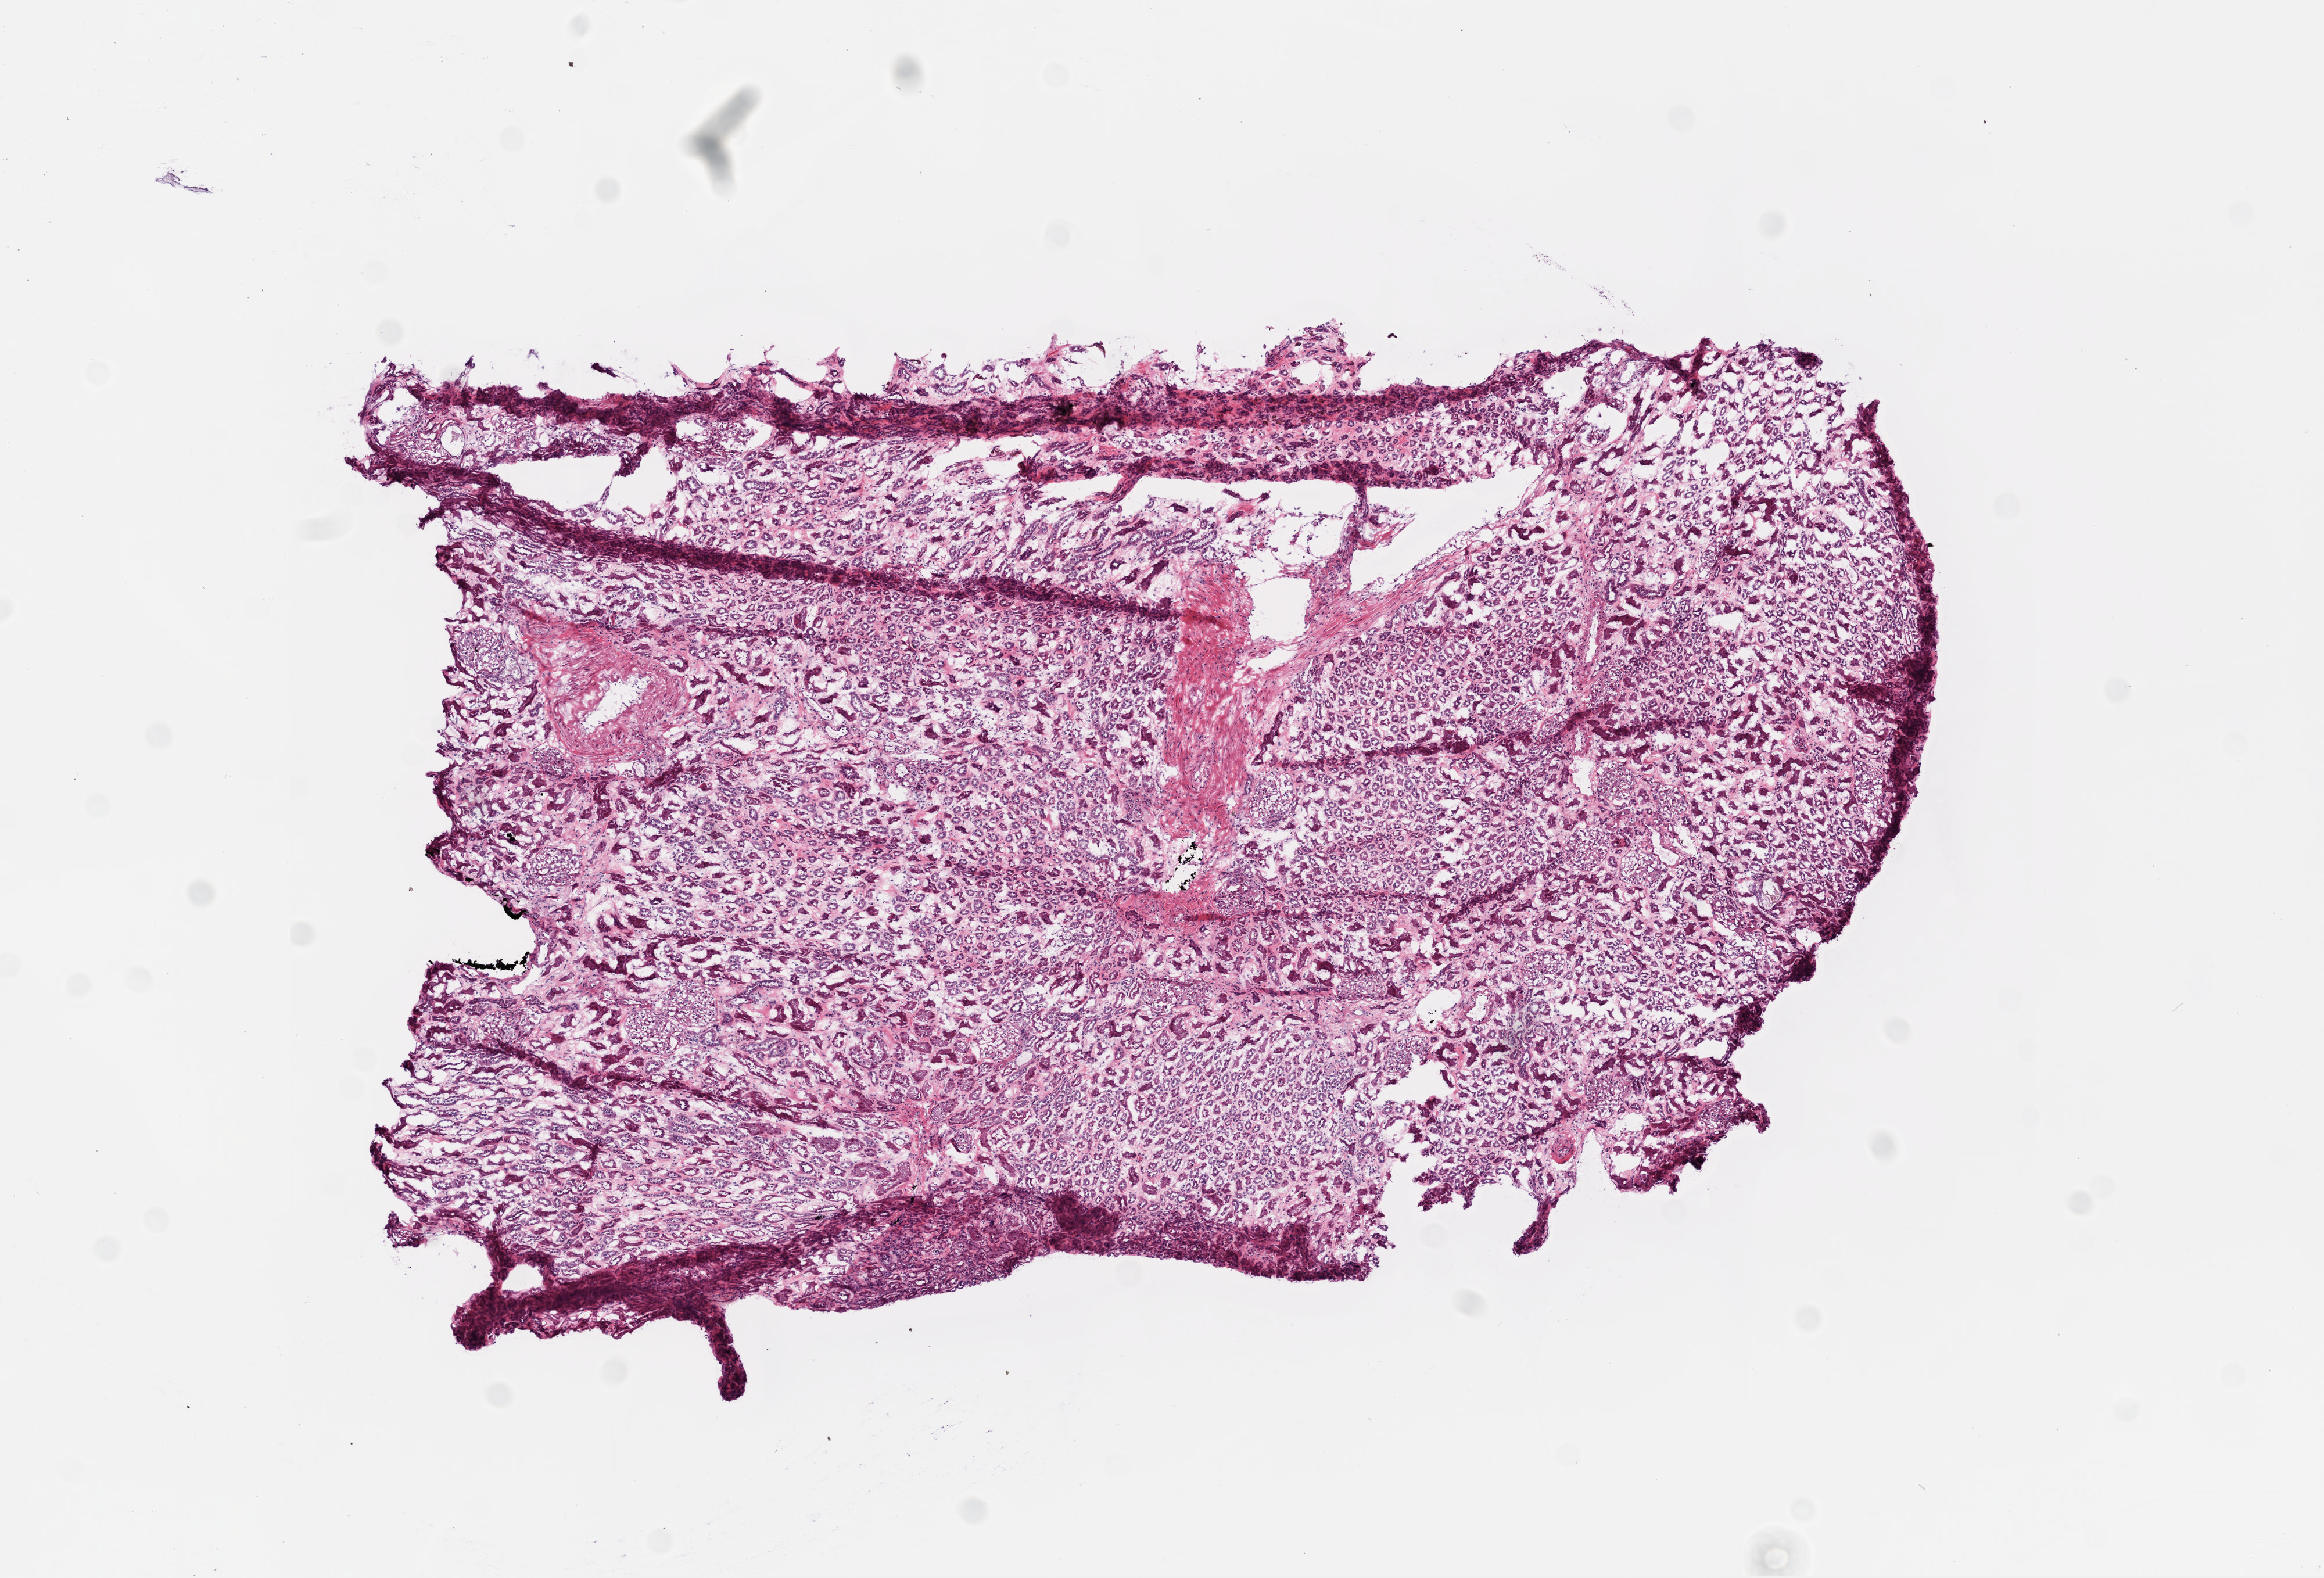
Whole-slide histology image, H&E-stained, low-resolution overview of the scanned area, about 8.0 x 5.4 mm (slide scanned at 20x), frozen section, kidney, solid tissue normal (non-tumour tissue) sample. Male, age 67 years at initial diagnosis.
This section: solid tissue normal sample (biorepository sample class). Patient diagnosis: Clear cell adenocarcinoma, NOS.